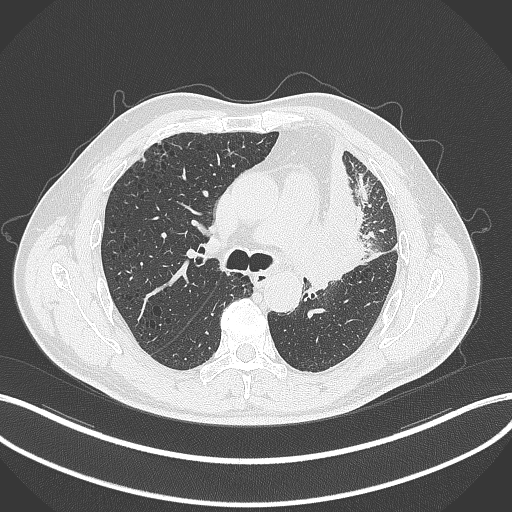
Chest CT, one axial slice; slice 191 of 297 in the series (ordered by position); lung window (W 1500 / L -600 HU); 1 mm slice thickness; 512 × 512 image matrix. Patient: male, 68 years. From the clinical record (not read from this slice): clinical TNM (as recorded): T3 N3 M1.
Annotated regions visible in this slice (bounding box drawn by a radiologist):
- lung tumour (recorded histology: adenocarcinoma): box from (x=314, y=158) to (x=378, y=291) px